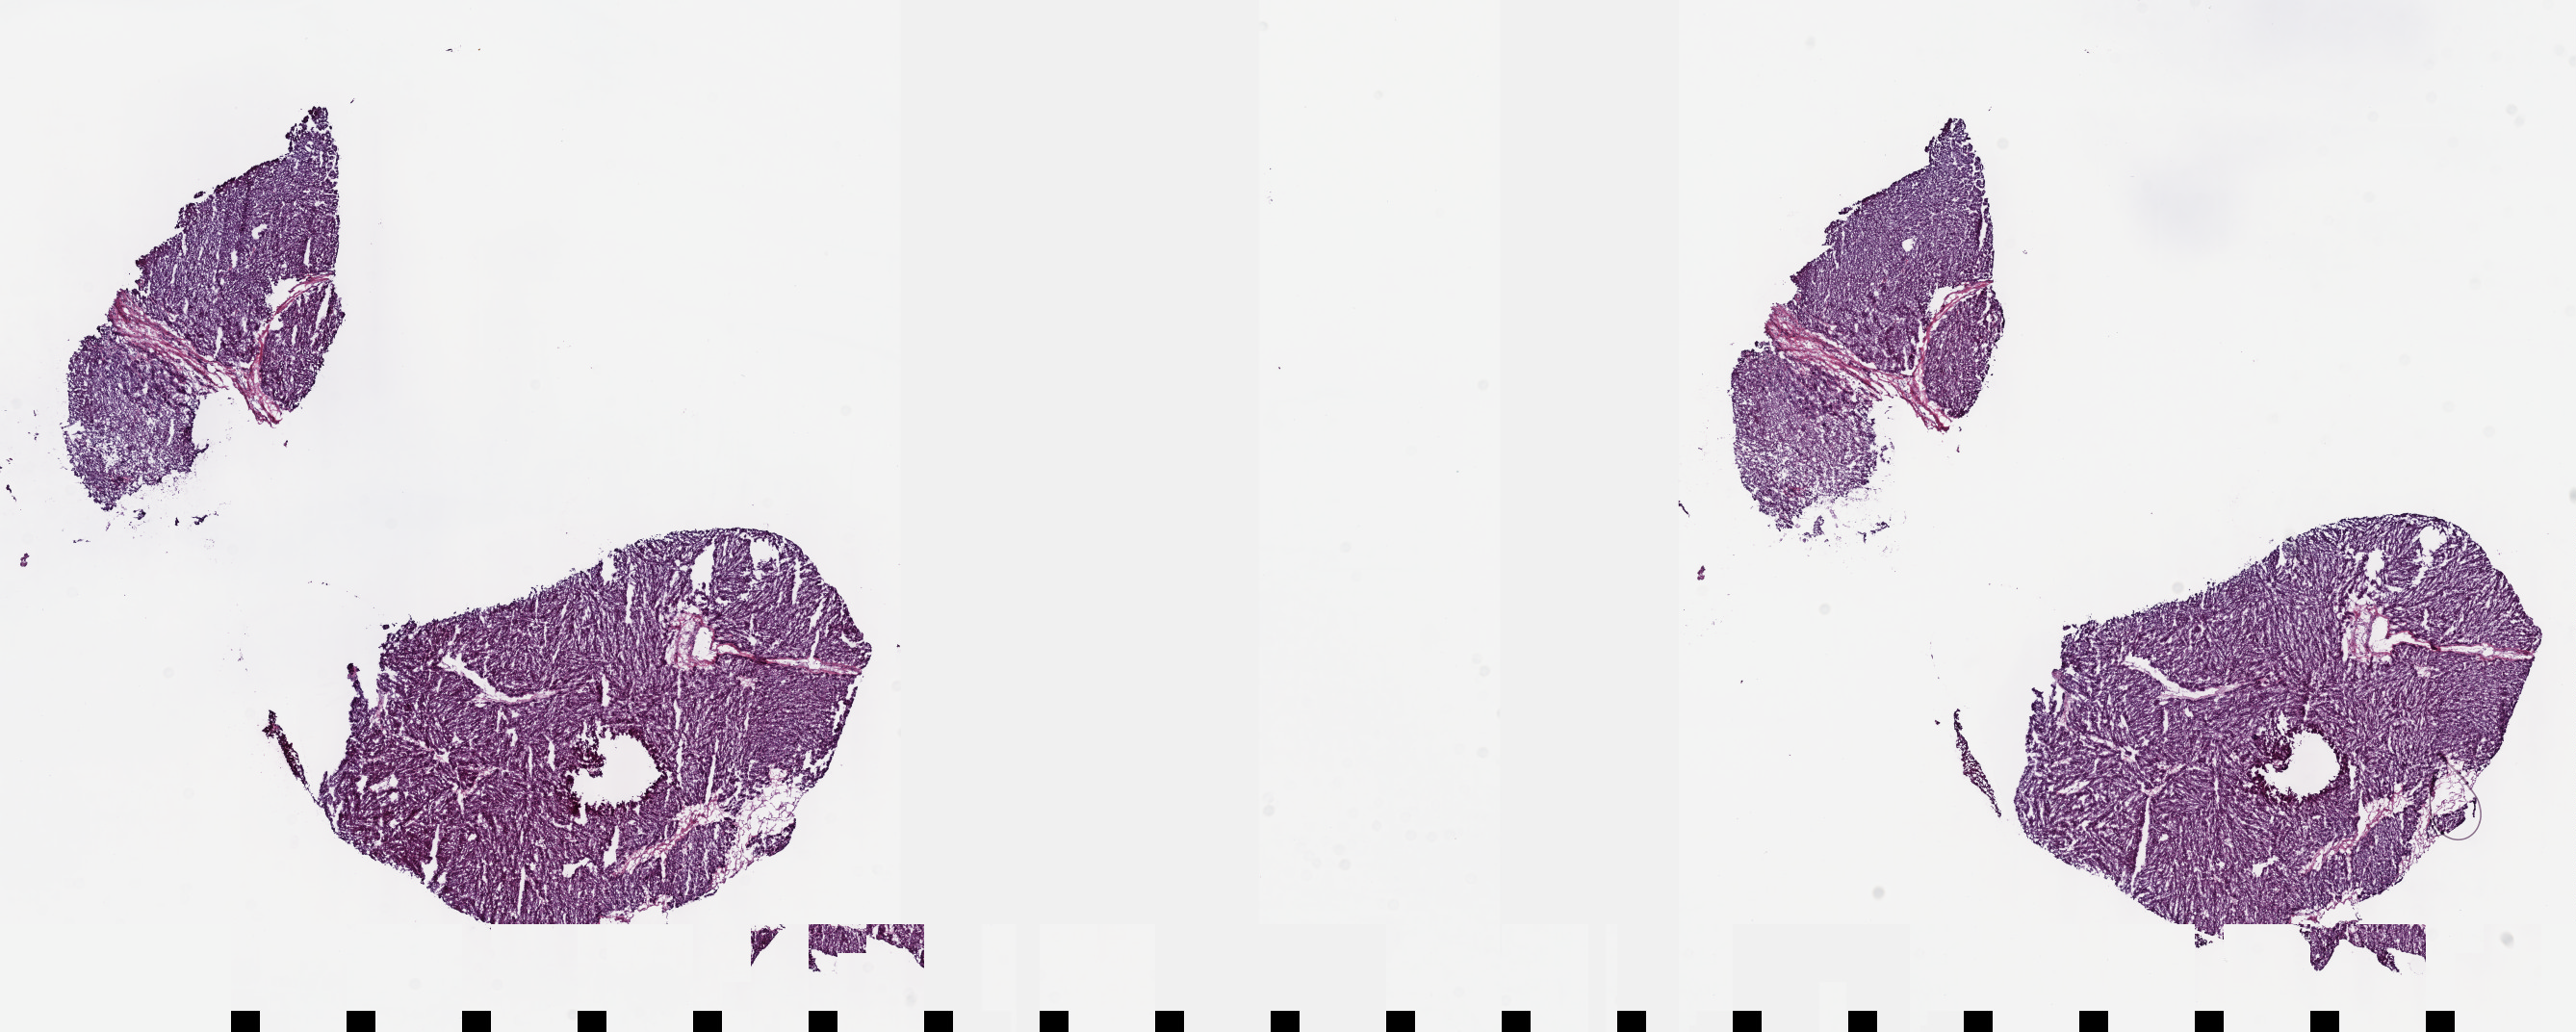
H&E whole-slide image — whole scanned area (about 21.6 x 8.7 mm) shown as a low-resolution overview. Frozen section from the top of the tissue portion. Primary tumour sample from the liver. Male patient; age at initial diagnosis 68 years. Histologic grade: G2 (moderately differentiated). Slide review estimates, as recorded: tumour cells 85%, tumour nuclei 85%, normal cells 0%, stromal cells 15%, necrosis 0%. Infiltration values recorded for this section: lymphocyte infiltration 3%, monocyte infiltration 1%, neutrophil infiltration 2%.
TNM: T1 N0 MX. AJCC pathologic stage: I. Histologic diagnosis: Hepatocellular carcinoma, NOS.